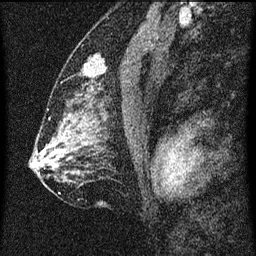
Breast MRI (dynamic contrast-enhanced), one sagittal slice; slice 38 of 60 in the series (ordered by position); dynamic contrast-enhanced series, image 2 of 3 at this slice position (ordered by acquisition); 1.5 T; TE 4.2 ms, TR 8 ms; 2 mm slice thickness; 256 × 256 image matrix. Patient: female, 52 years.
Structures marked on this image (semi-automatic segmentation, software-assisted and operator-edited):
- analysis volume of interest (the breast-tissue region the enhancement analysis was run in; not a lesion): bounding box [x1, y1, x2, y2] px = [72, 50, 116, 101]
- tumour enhancement mask (voxels above the 70 % enhancement threshold inside the analysis volume of interest): [83, 56, 96, 73]